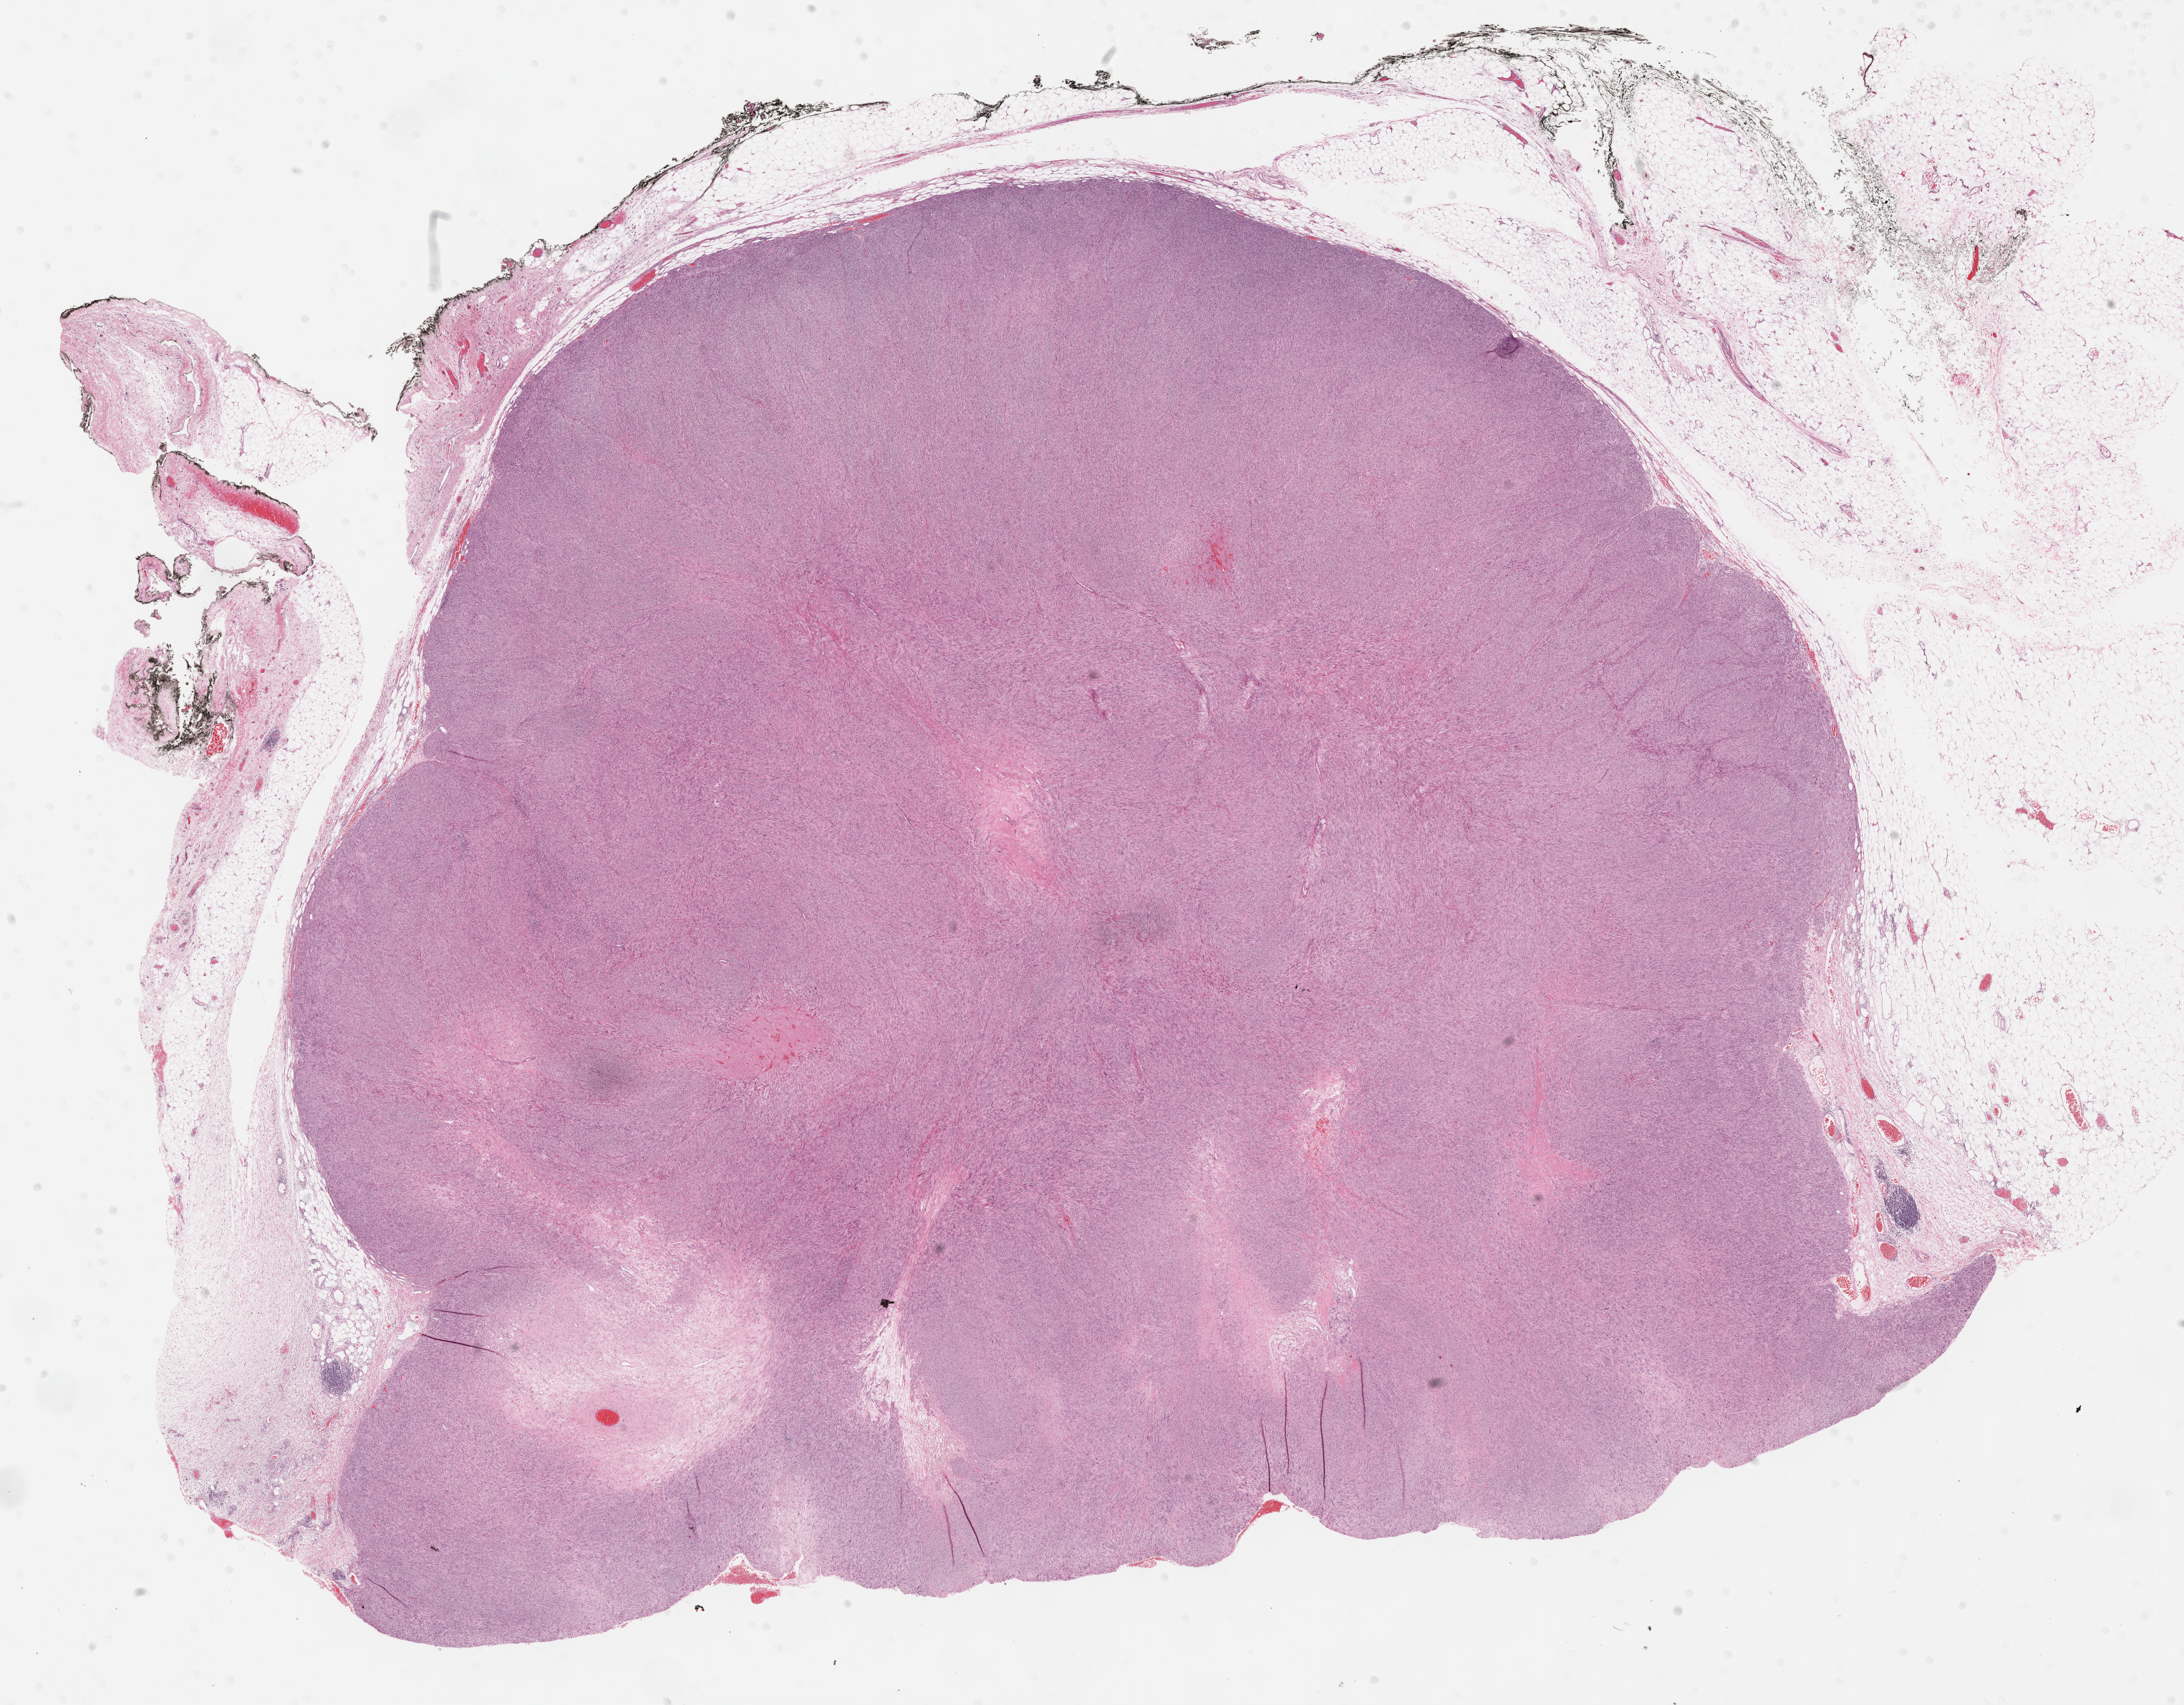
Digitized H&E tissue section (whole slide), low-resolution overview of the scanned area, about 24.7 x 19.3 mm (acquisition: 40x scan). FFPE section. Sample: primary tumour, retroperitoneum and peritoneum. Male, age 61 years at initial diagnosis.
• diagnosis: Leiomyosarcoma, NOS (retroperitoneum)